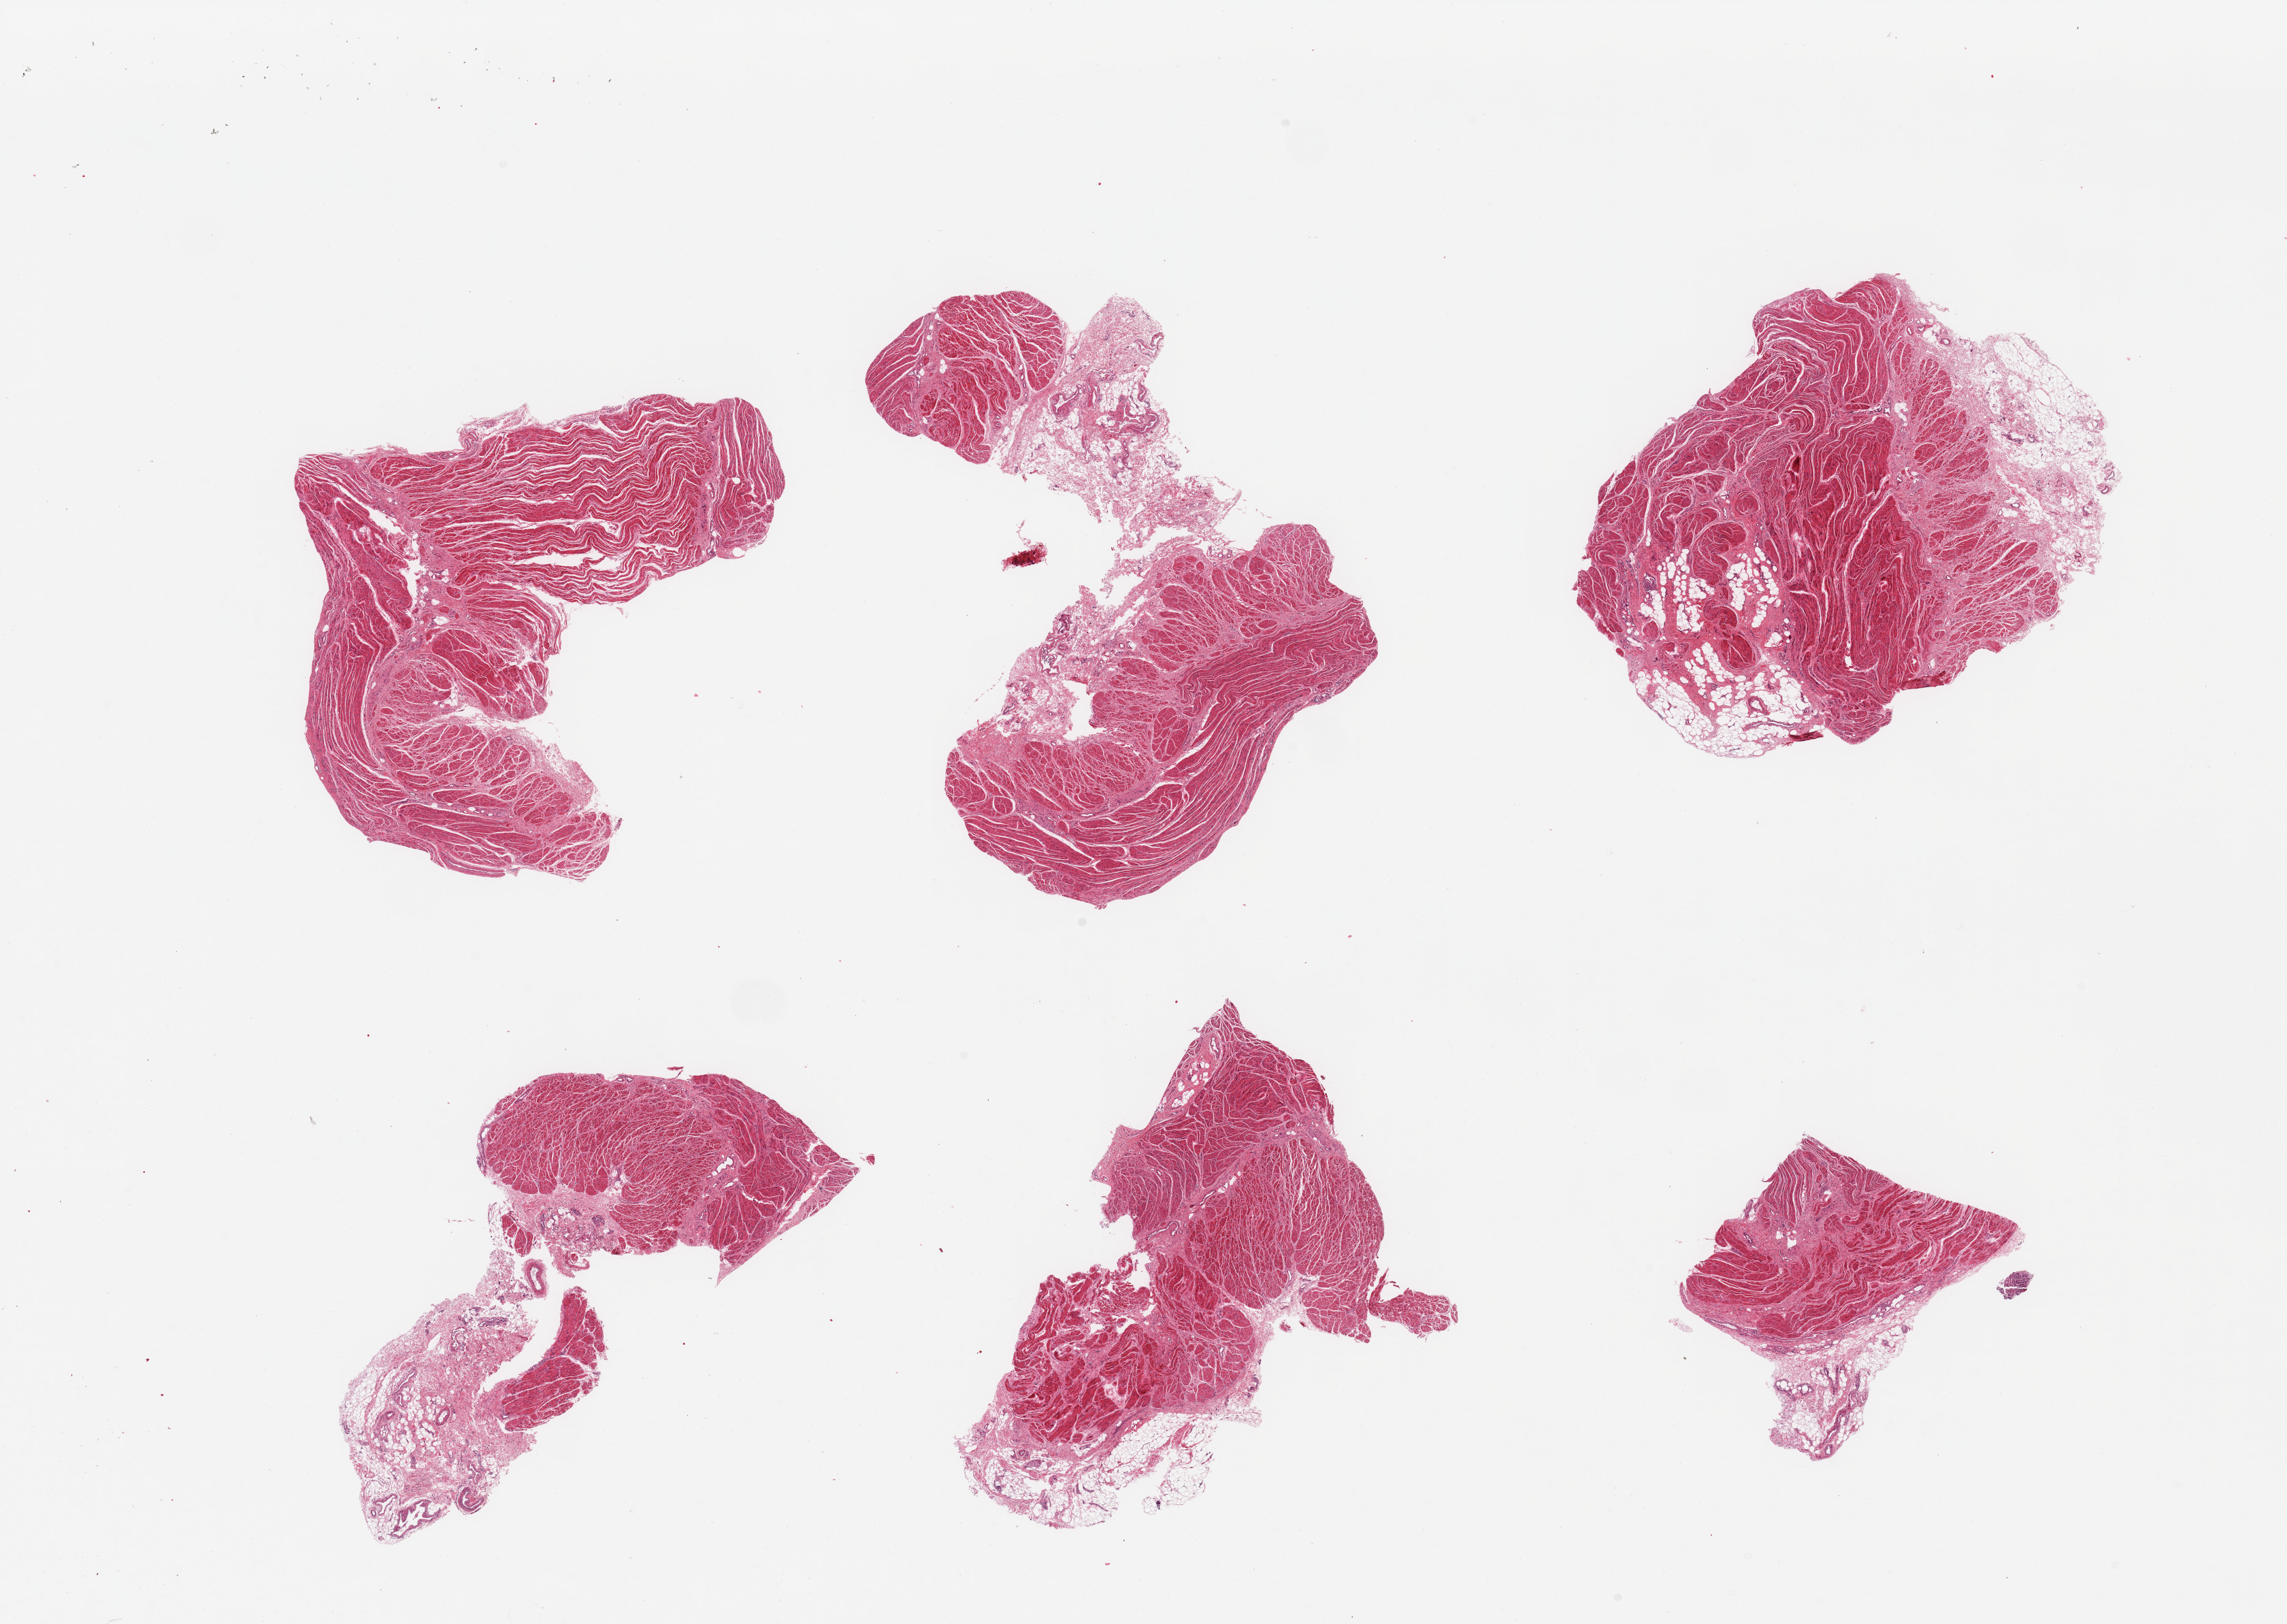
Hematoxylin and eosin (H&E) whole-slide image, a low-resolution overview of the entire scanned area, about 26.6 x 18.9 mm (acquisition: 20x scan). PAXgene-fixed paraffin-embedded (PFPE) section. Sampled site (target tissue): gastroesophageal junction. Donor tissue sample. Male donor.
Review note (as recorded): 6 pieces; muscularis, includes residual fat/fibrous/vascular tissue.